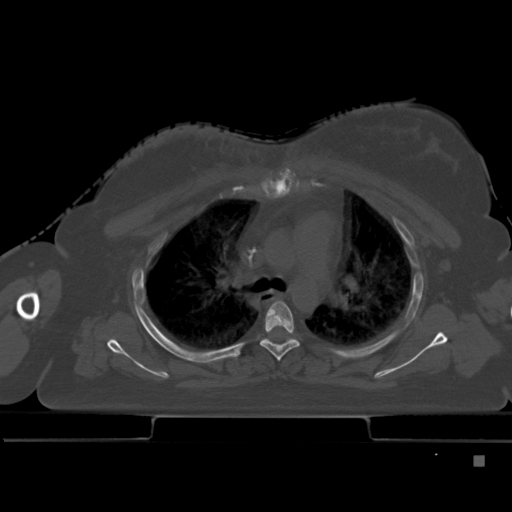
CT including the spine, one axial slice; slice 331 of 495 in the series (ordered by position); bone window (W 1800 / L 400 HU); 1.5 mm slice thickness; 512 × 512 image matrix, field of view 404 × 404 mm. Female patient, age 33 years. Case-level facts recorded for this patient, not image findings: primary cancer: breast; vertebrae with lytic lesions (as recorded): T1.
Annotated regions visible in this slice (semi-automatically segmented with operator editing):
- T4 vertebra: bounding box [x1, y1, x2, y2] px = [260, 301, 300, 361]
- T5 vertebra: [263, 338, 295, 344]